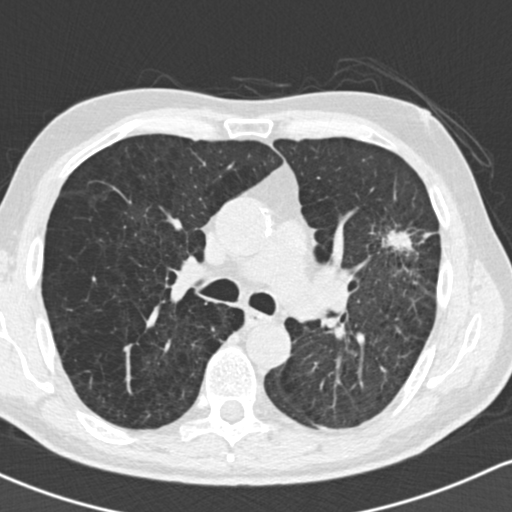
Low-dose screening chest CT, axial slice, baseline screening round, lung window (W 1500 / L -600 HU), 2 mm slice thickness, standard (soft-tissue) reconstruction kernel (B30f), slice 68 of 162 in the series. Male, age 61 years at enrolment. Former smoker at enrolment.
Expert-annotated lung lesion, box from (x=357, y=188) to (x=458, y=297) px. Reader record for this screening exam (exam-level; its link to the box is not recorded): non-calcified nodule or mass ≥4 mm, left upper lobe, 35 × 35 mm, spiculated (stellate) margins, soft tissue attenuation. Lung cancer was diagnosed 19 days after this screen: adenocarcinoma, NOS, left upper lobe, well differentiated (G1), stage IIIA (AJCC 6th edition), 45 mm at pathology.